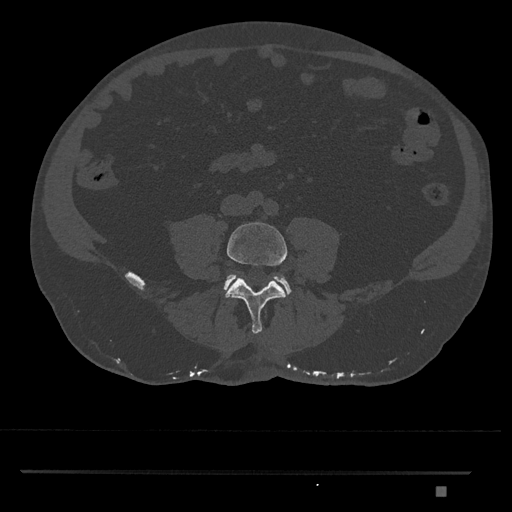
CT including the spine, one axial slice; position 601 of 1134 along the scan axis; reconstruction kernel Br40s/3; bone window (W 1800 / L 400 HU); 0.5 mm slice thickness; 512 × 512 image matrix, field of view 429 × 429 mm. Male patient, age 65 years. From the clinical record (not read from this slice): primary cancer: prostate.
Outlined on this slice (semi-automatically segmented with operator editing):
- L4 vertebra: bounding box [x1, y1, x2, y2] px = [225, 222, 287, 334]
- L5 vertebra: [223, 274, 291, 295]